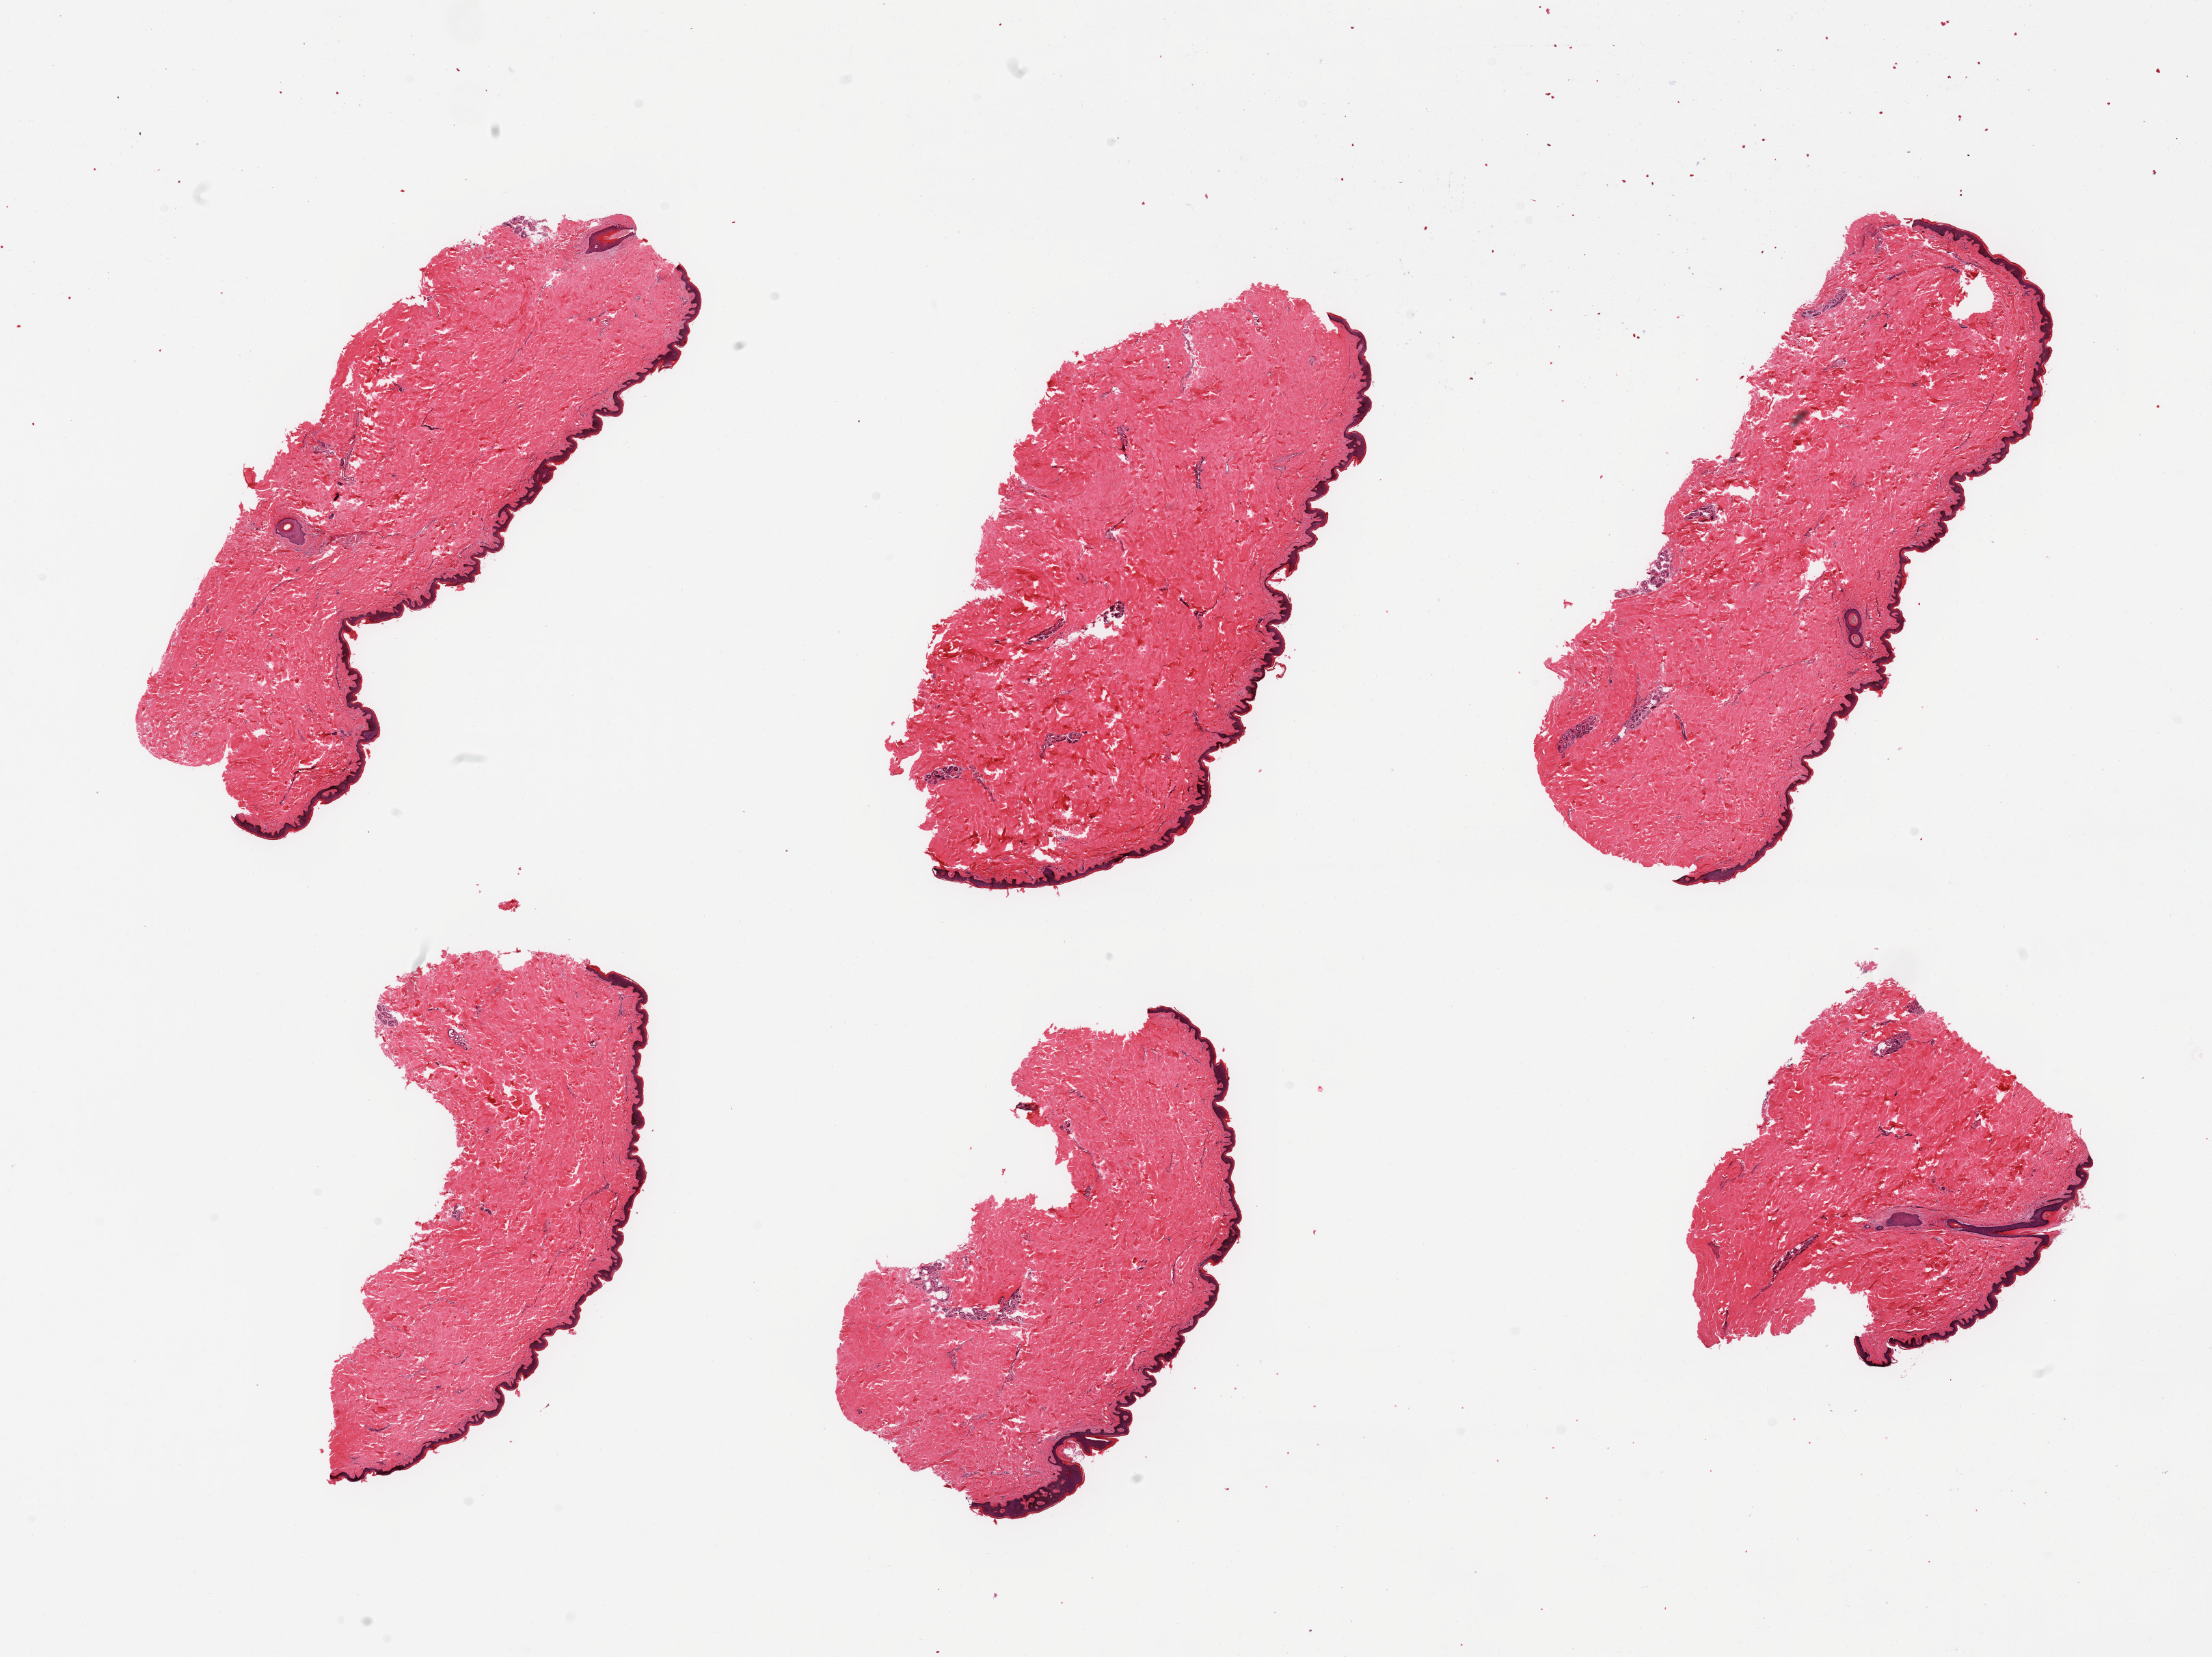
Digitized hematoxylin and eosin (H&E)-stained section, whole scanned area (about 25.6 x 19.2 mm, from a 20x scan) shown as a low-resolution overview, PAXgene-fixed paraffin-embedded (PFPE) section, target tissue: skin of suprapubic region, donor tissue sample. Donor: male.
Pathologist's review note for this sample: 6 pieces, no adherent dermal fat, squamous epithelium is ~50 microns.